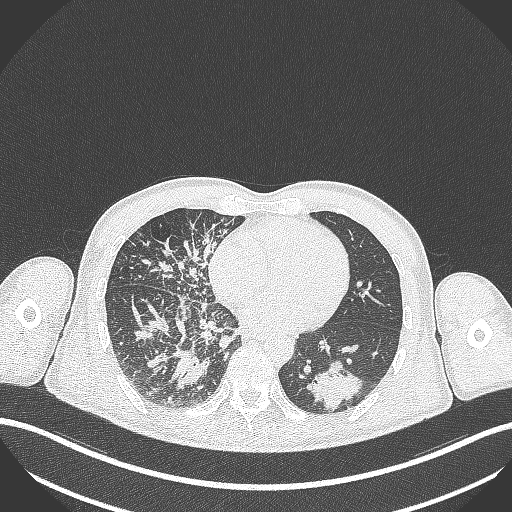
Chest CT, one axial slice; slice 118 of 348 in the series (ordered by position); reconstruction kernel B70f; lung window (W 1500 / L -600 HU); 1 mm slice thickness; 512 × 512 image matrix, field of view 400 × 400 mm. Male patient, age 49 years. Case-level facts recorded for this patient, not image findings: clinical TNM (as recorded): T2b N1 M0.
Annotated regions visible in this slice (rectangle marked by the reading radiologist):
- lung tumour (recorded histology: adenocarcinoma): bounding box <304,359,366,411> (left, top, right, bottom; pixels)